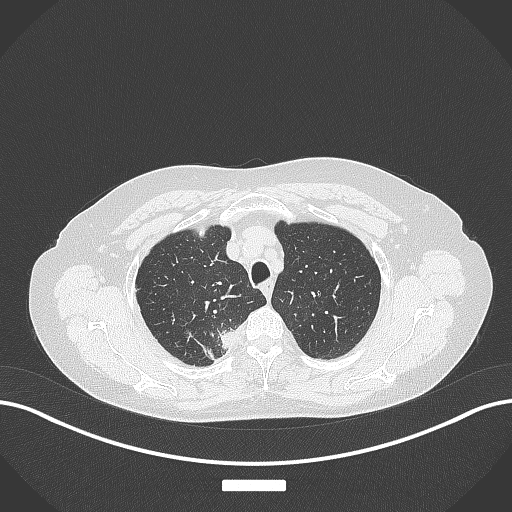
Chest CT, one axial slice; slice 321 of 357 in the series (ordered by position); reconstruction kernel B70f; lung window (W 1500 / L -600 HU); 1 mm slice thickness; 512 × 512 image matrix, field of view 400 × 400 mm. Patient: female, 62 years. Case-level facts recorded for this patient, not image findings: clinical TNM (as recorded): T1c N1 M0.
Outlined on this slice (bounding box drawn by a radiologist):
- lung tumour (recorded histology: squamous cell carcinoma): bounding box (x1, y1, x2, y2) in pixels: (215, 328, 240, 350)